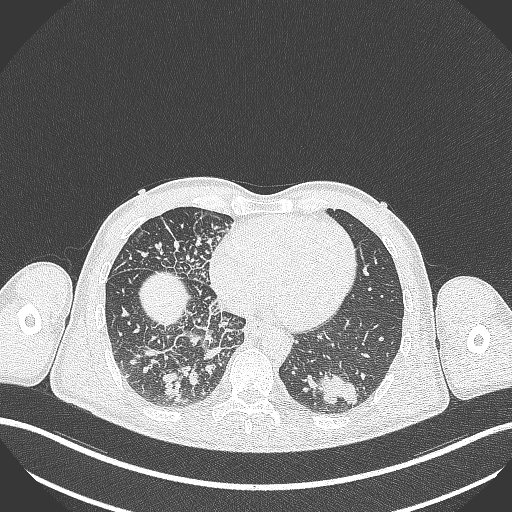
Chest CT, one axial slice; position 99 of 348 along the scan axis; 120 kVp; lung window (W 1500 / L -600 HU); 1 mm slice thickness; 512 × 512 image matrix, field of view 400 × 400 mm. Patient: male, 49 years. From the clinical record (not read from this slice): clinical TNM (as recorded): T2b N1 M0.
Annotated regions visible in this slice (bounding box drawn by a radiologist):
- lung tumour (recorded histology: adenocarcinoma): bounding box <318,367,367,409> (left, top, right, bottom; pixels)